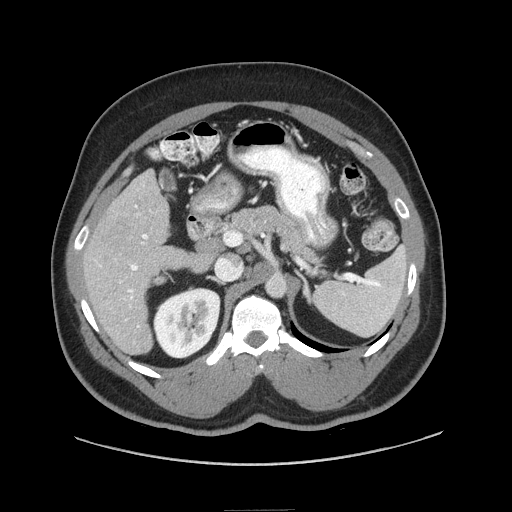
Contrast-enhanced abdominal CT (liver protocol), one axial slice; 140 kVp; soft-tissue window (W 400 / L 40 HU); 2.5 mm slice thickness; 512 × 512 image matrix, field of view 440 × 440 mm. From the clinical record (not read from this slice): diagnosis: hepatocellular carcinoma (patient treated with transarterial chemoembolisation; whether this scan precedes or follows treatment is not stated here); TNM stage (as recorded): Stage-II; Child-Pugh class: A; tumour differentiation: moderately differentiated; tumour nodularity: uninodular.
Outlined on this slice (semi-automatic segmentation, software-assisted and operator-edited):
- liver parenchyma outside the tumour (the mass and vessels are separate outlines, so this box may not span the whole liver): box from (x=82, y=170) to (x=212, y=354) px
- liver vessels: (x=94, y=205)–(x=148, y=328)